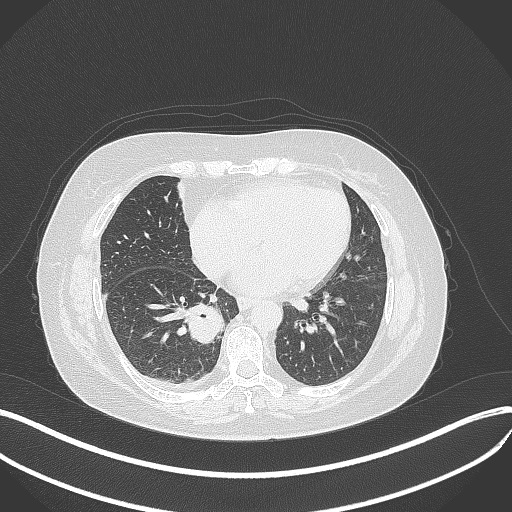
Chest CT, one axial slice; position 138 of 381 along the scan axis; reconstruction kernel B70f; 120 kVp; lung window (W 1500 / L -600 HU); 1 mm slice thickness; 512 × 512 image matrix. Patient: female, 56 years. From the clinical record (not read from this slice): clinical TNM (as recorded): T2b N1 M0; histopathological grade: G3.
Outlined on this slice (rectangle marked by the reading radiologist):
- lung tumour (recorded histology: small cell carcinoma): box from (x=189, y=302) to (x=228, y=348) px